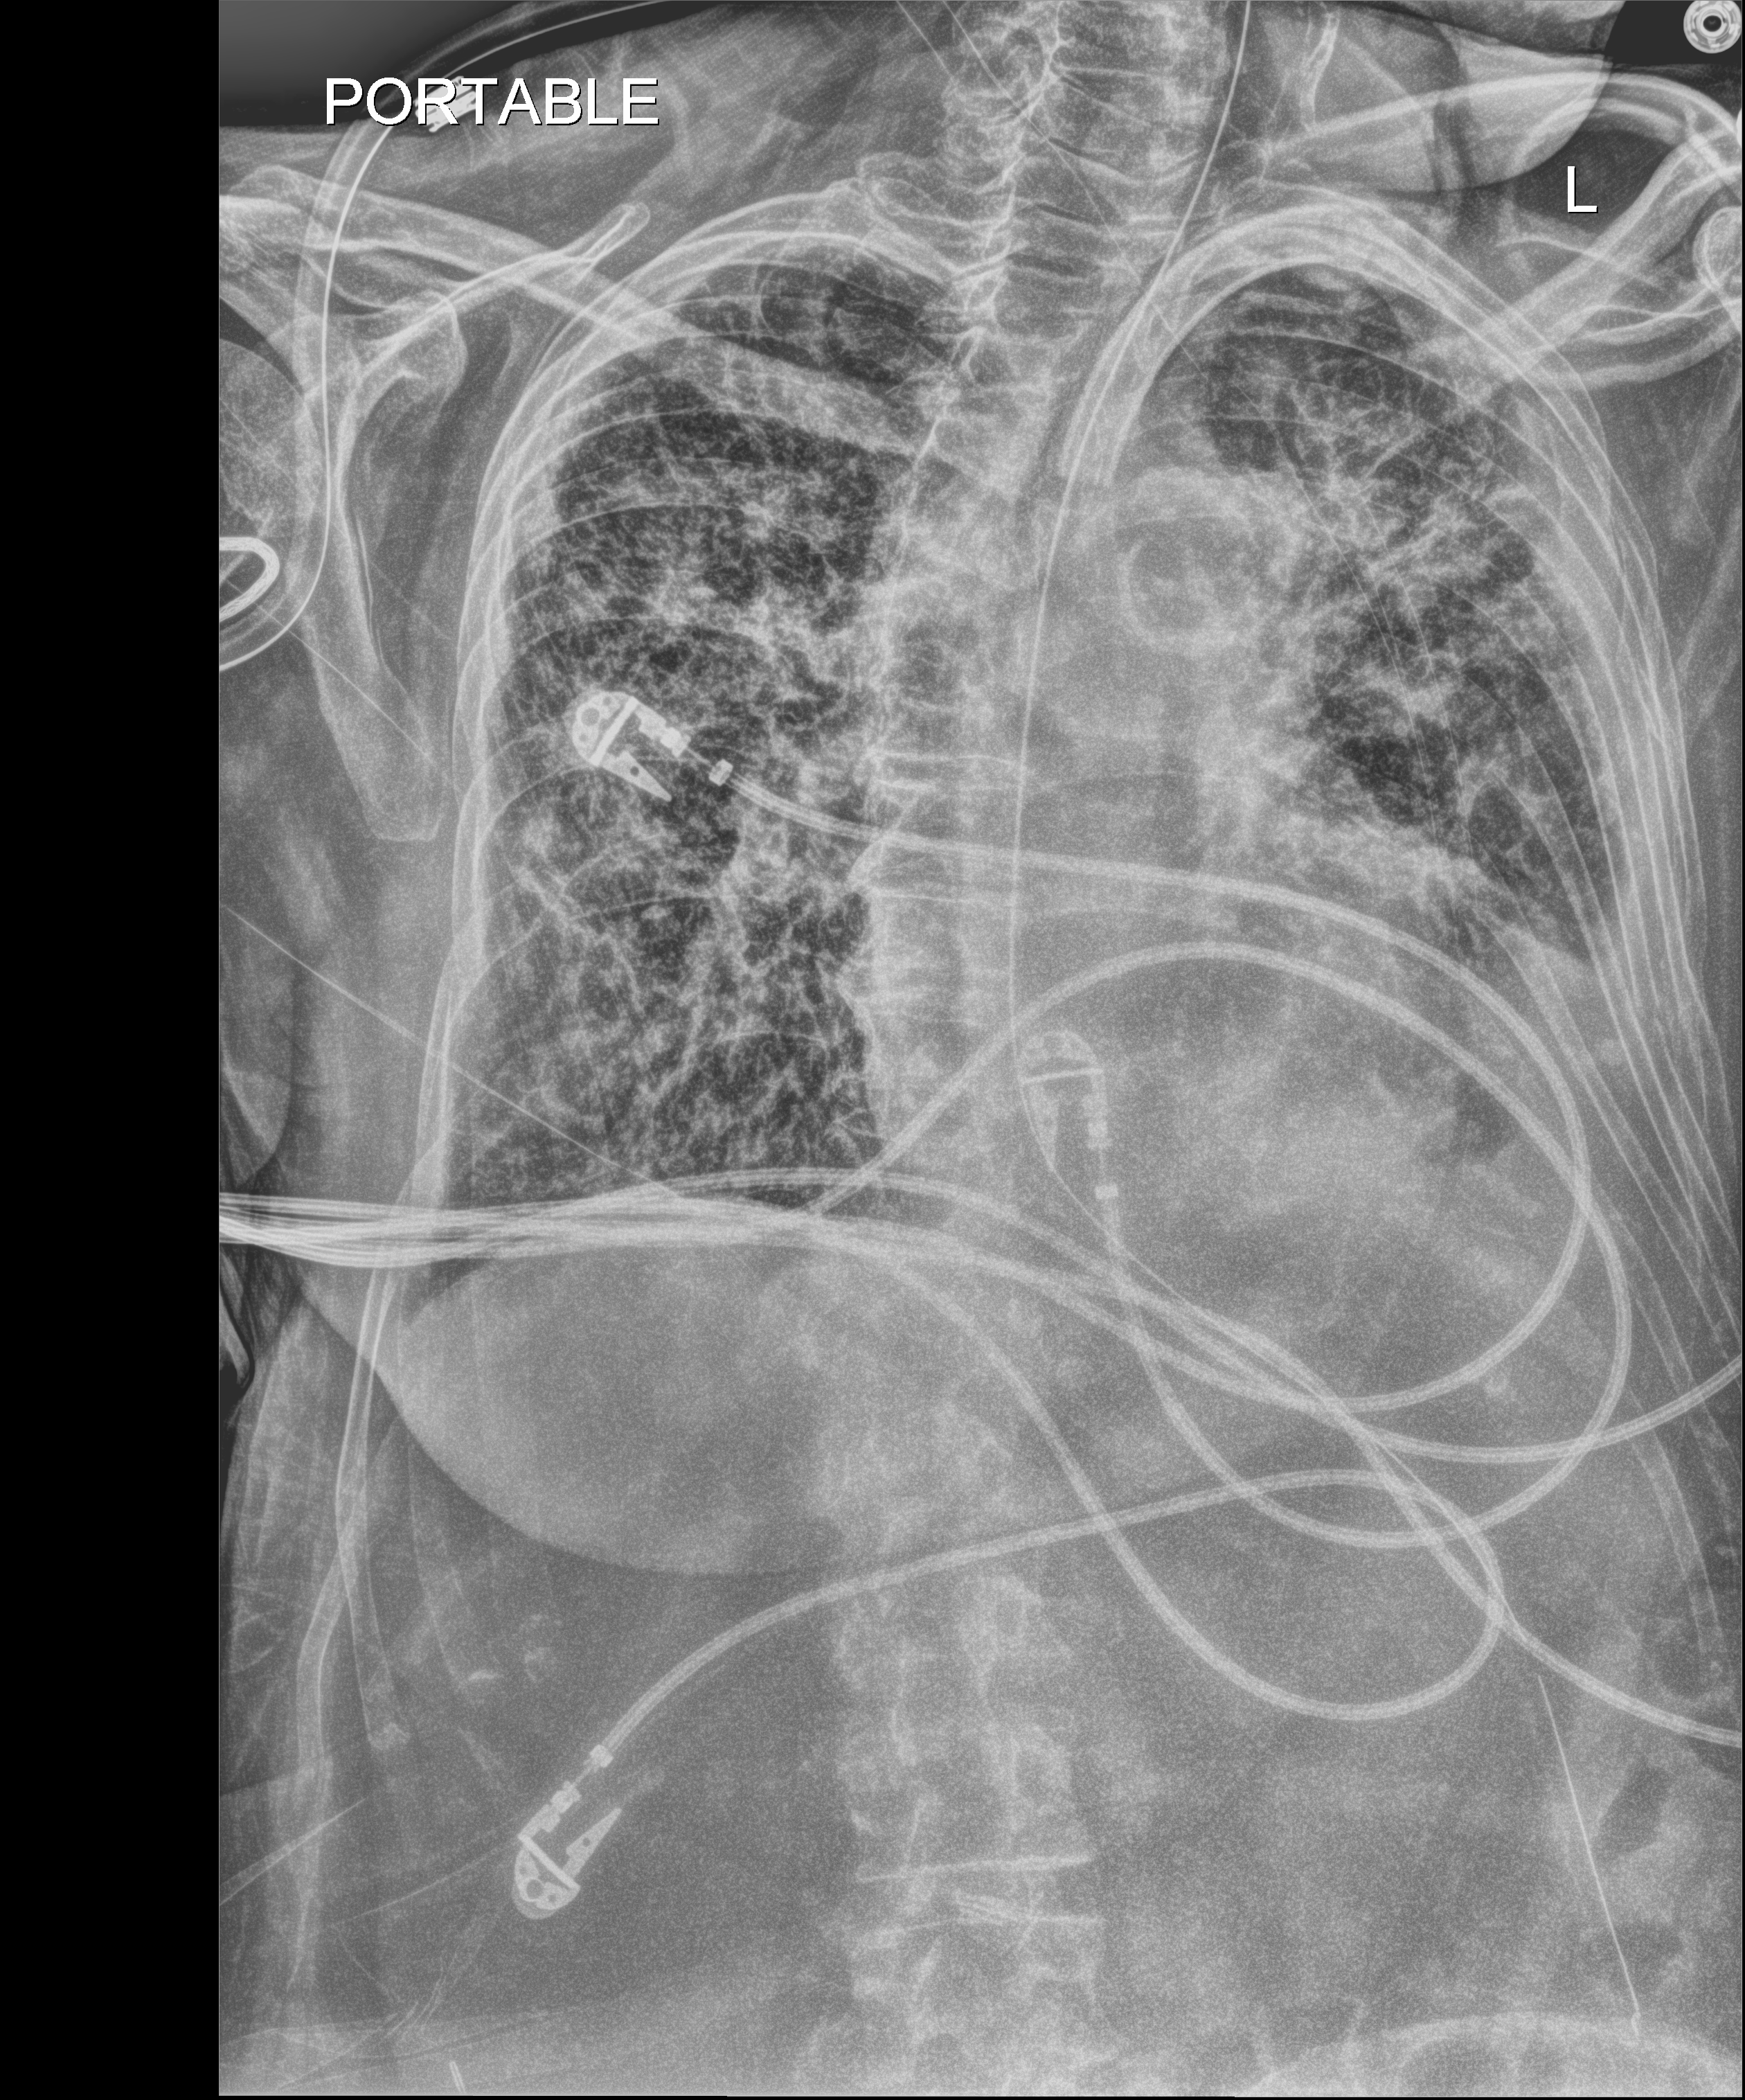
Bedside chest radiograph (digital radiography); anteroposterior (AP) projection. Female patient hospitalised with COVID-19, age 75–90 years.
Admission-level facts for this patient (not findings on this image; timing relative to this image not recorded): length of hospital stay: 70 days.